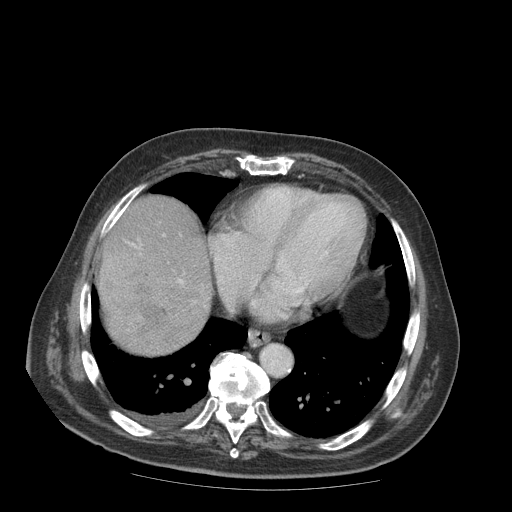
Contrast-enhanced abdominal CT (liver protocol), one axial slice. Slice 84 of 99 in the series (ordered by position). Reconstruction kernel STANDARD. Soft-tissue window (W 400 / L 40 HU). 2.5 mm slice thickness. 512 × 512 image matrix. Case-level facts recorded for this patient, not image findings: diagnosis: hepatocellular carcinoma (patient treated with transarterial chemoembolisation; whether this scan precedes or follows treatment is not stated here); TNM stage (as recorded): Stage-IIIB; Child-Pugh class: A; tumour differentiation: well differentiated; tumour nodularity: multinodular.
Structures marked on this image (semi-automatically segmented with operator editing):
- abdominal aorta: bounding box [x1, y1, x2, y2] px = [260, 343, 292, 376]
- liver parenchyma outside the tumour (the mass and vessels are separate outlines, so this box may not span the whole liver): [96, 194, 210, 317]
- mass: [99, 251, 207, 356]
- liver vessels: [132, 244, 184, 284]